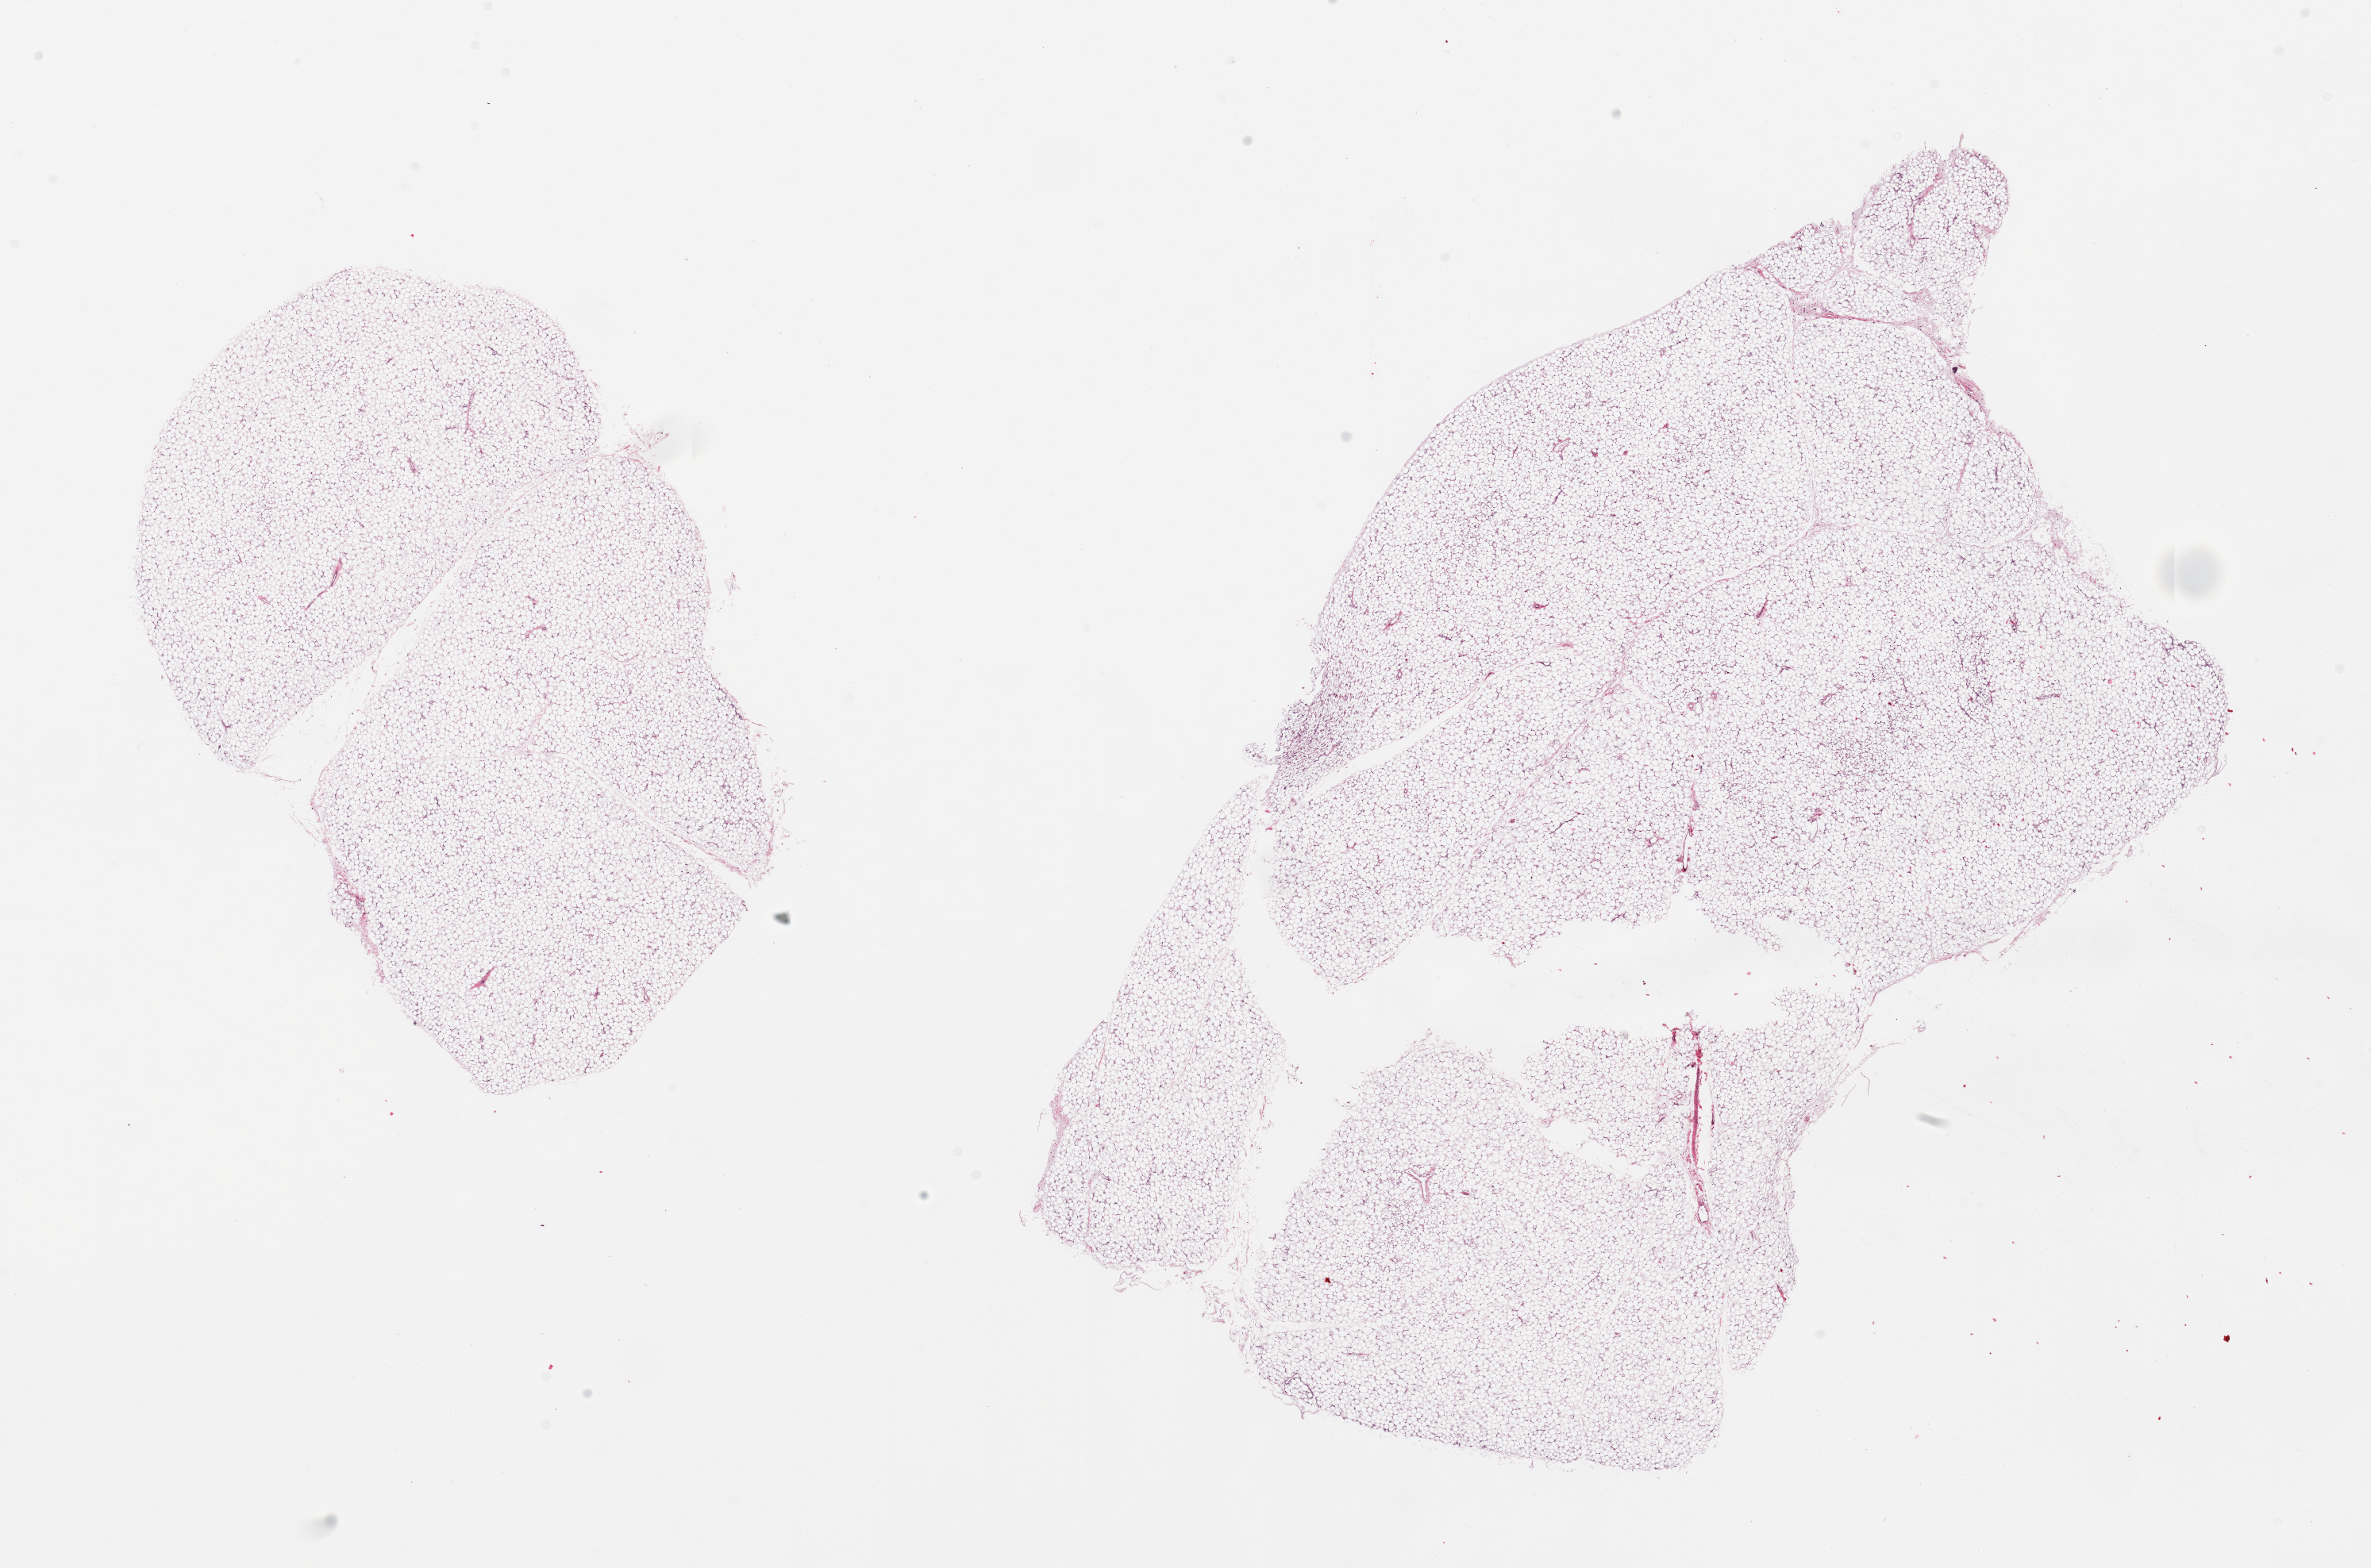
Whole-slide image, hematoxylin and eosin (H&E) stain, low-resolution overview of the scanned area, about 23.6 x 15.6 mm (slide scanned at 20x); PAXgene-fixed, paraffin-embedded tissue; section of adrenal gland (target tissue); donor tissue sample. Donor: male.
Review note (as recorded): 2 pieces; all adipose tissue, no adrenal.